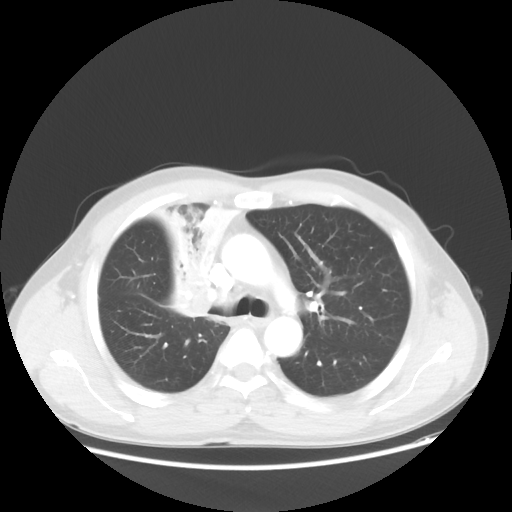
Chest CT, one axial slice; slice 36 of 56 in the series (ordered by position); lung window (W 1500 / L -600 HU); 5 mm slice thickness; 512 × 512 image matrix, field of view 398 × 398 mm. Male patient, age 60 years. From the clinical record (not read from this slice): clinical TNM (as recorded): T2a N1 M0.
Annotated regions visible in this slice (bounding box drawn by a radiologist):
- lung tumour (recorded histology: squamous cell carcinoma): bounding box <151,198,232,319> (left, top, right, bottom; pixels)